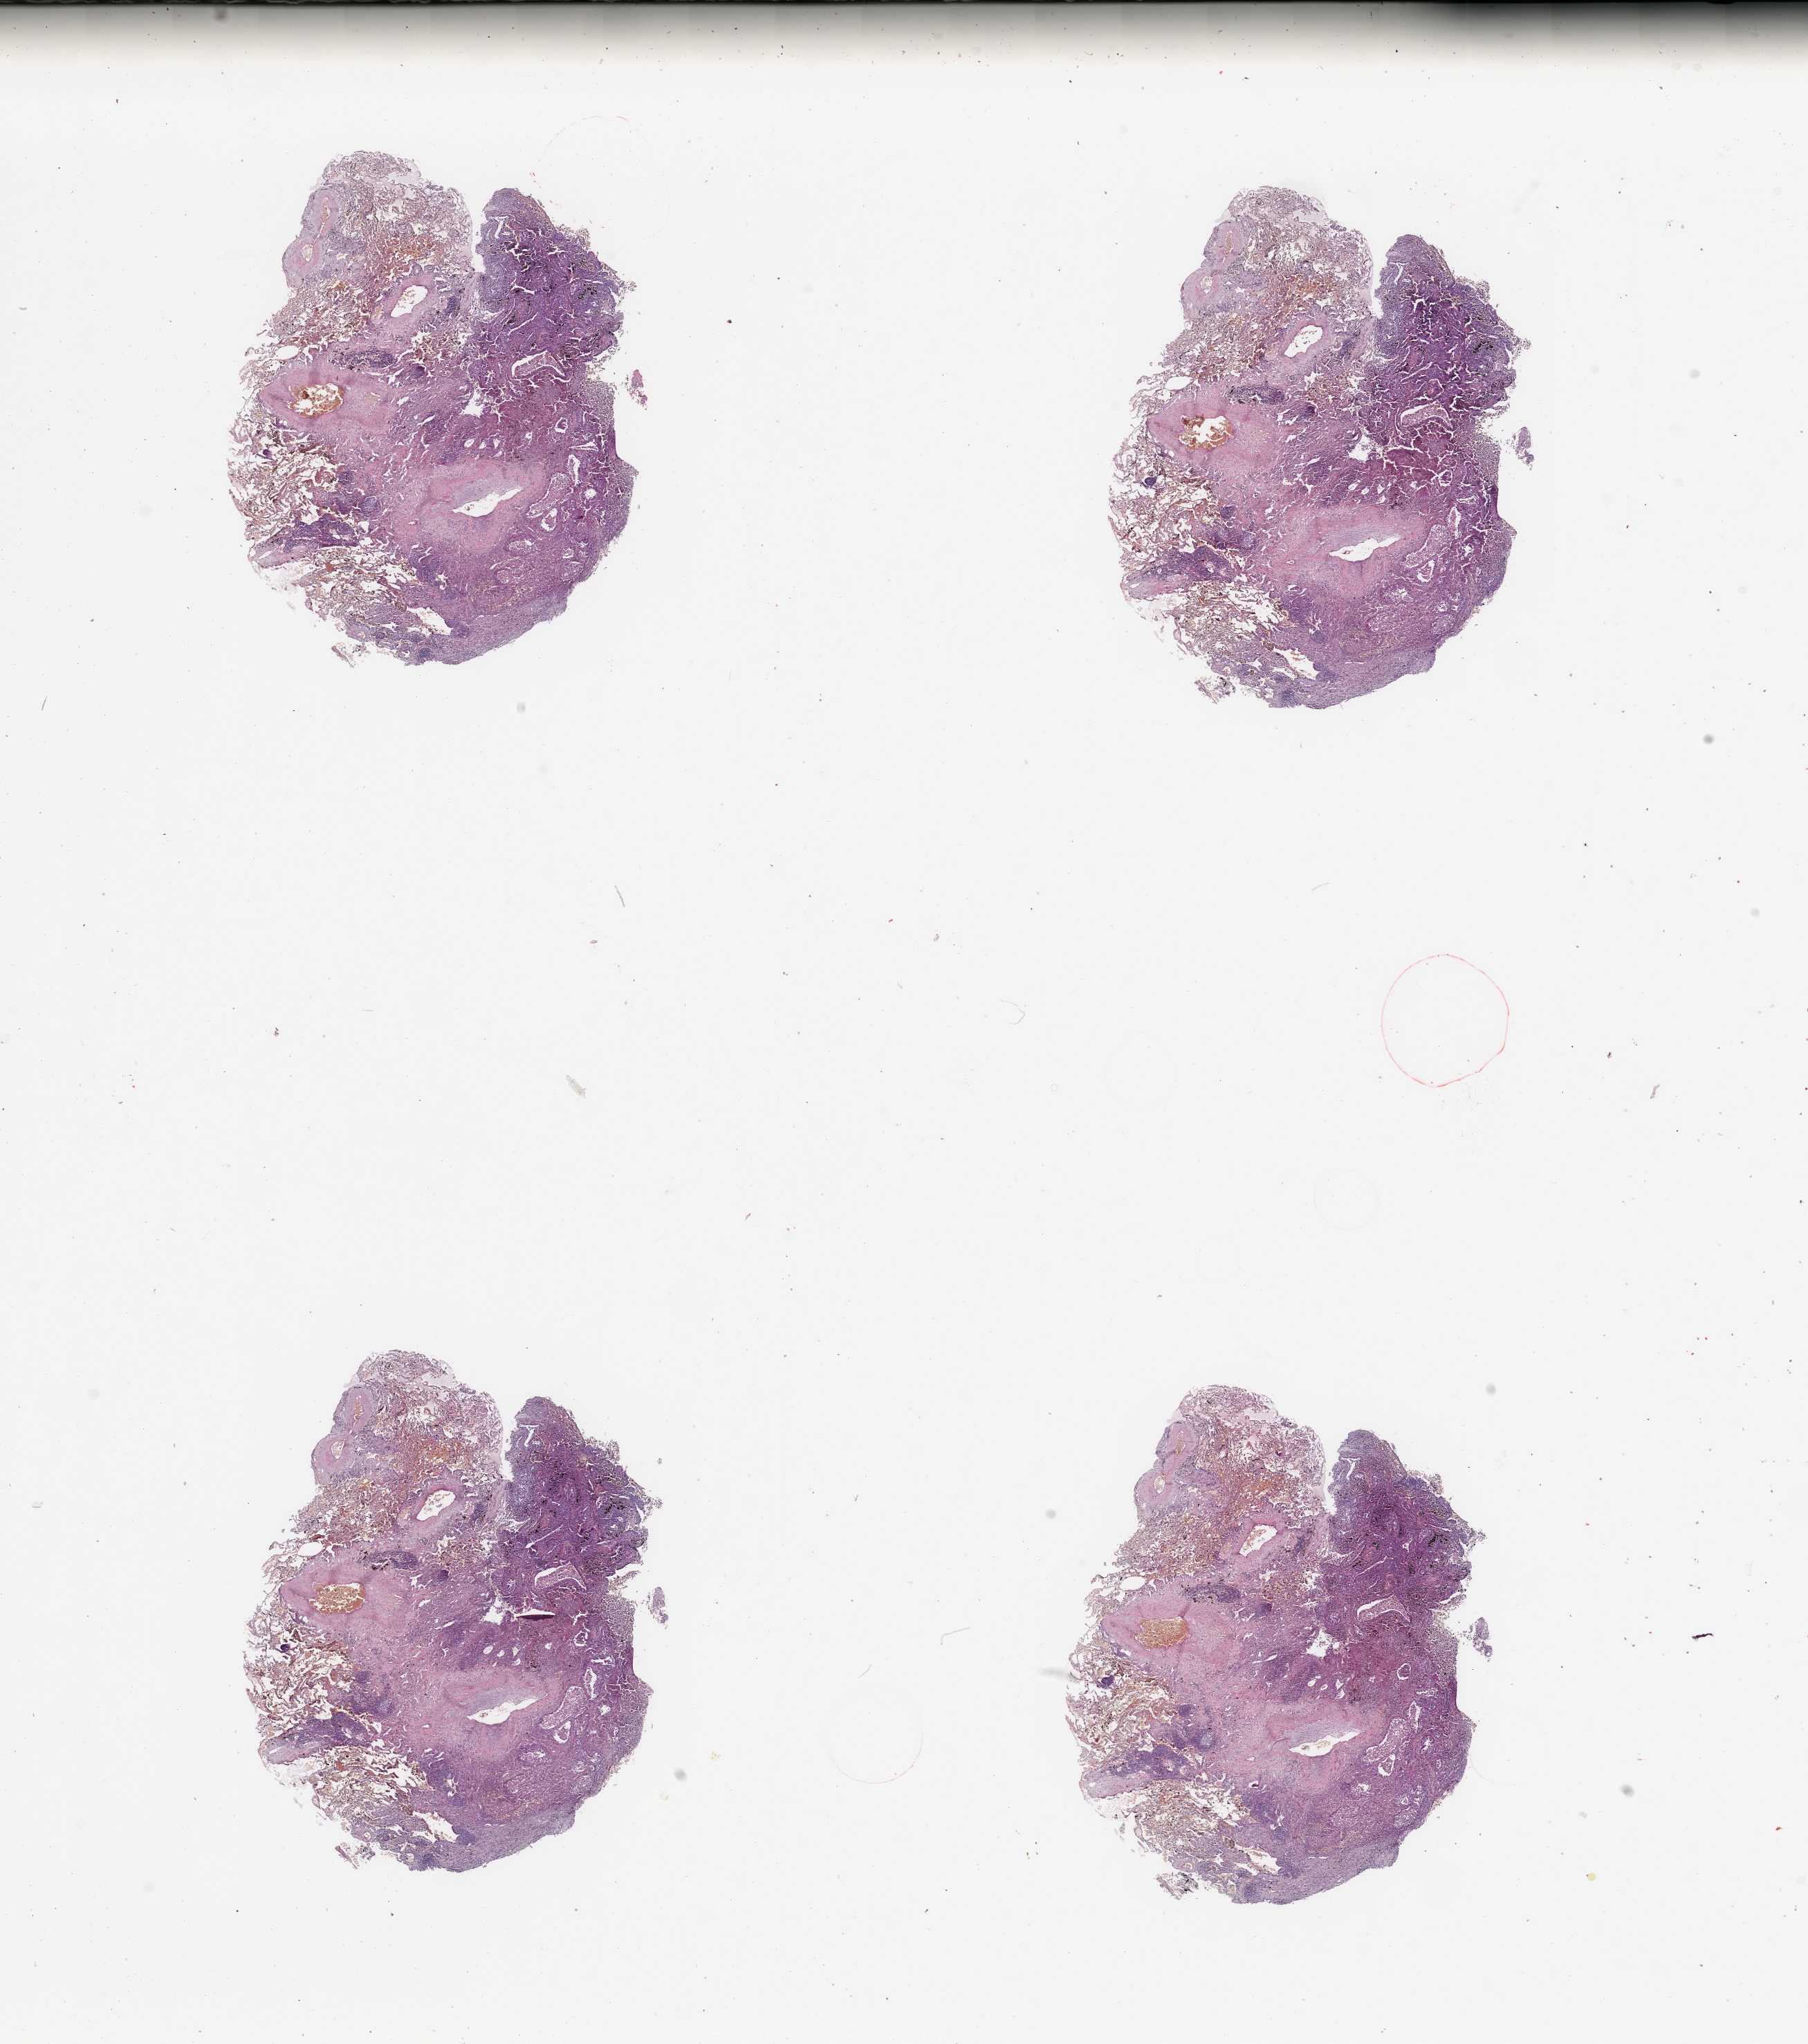
Whole-slide histology image, H&E-stained — low-resolution overview of the scanned area, about 20.7 x 23.4 mm (acquisition: 20x scan). Lung, tumour tissue. Male, 69 y/o.
Histologic diagnosis: Adenocarcinoma, NOS.